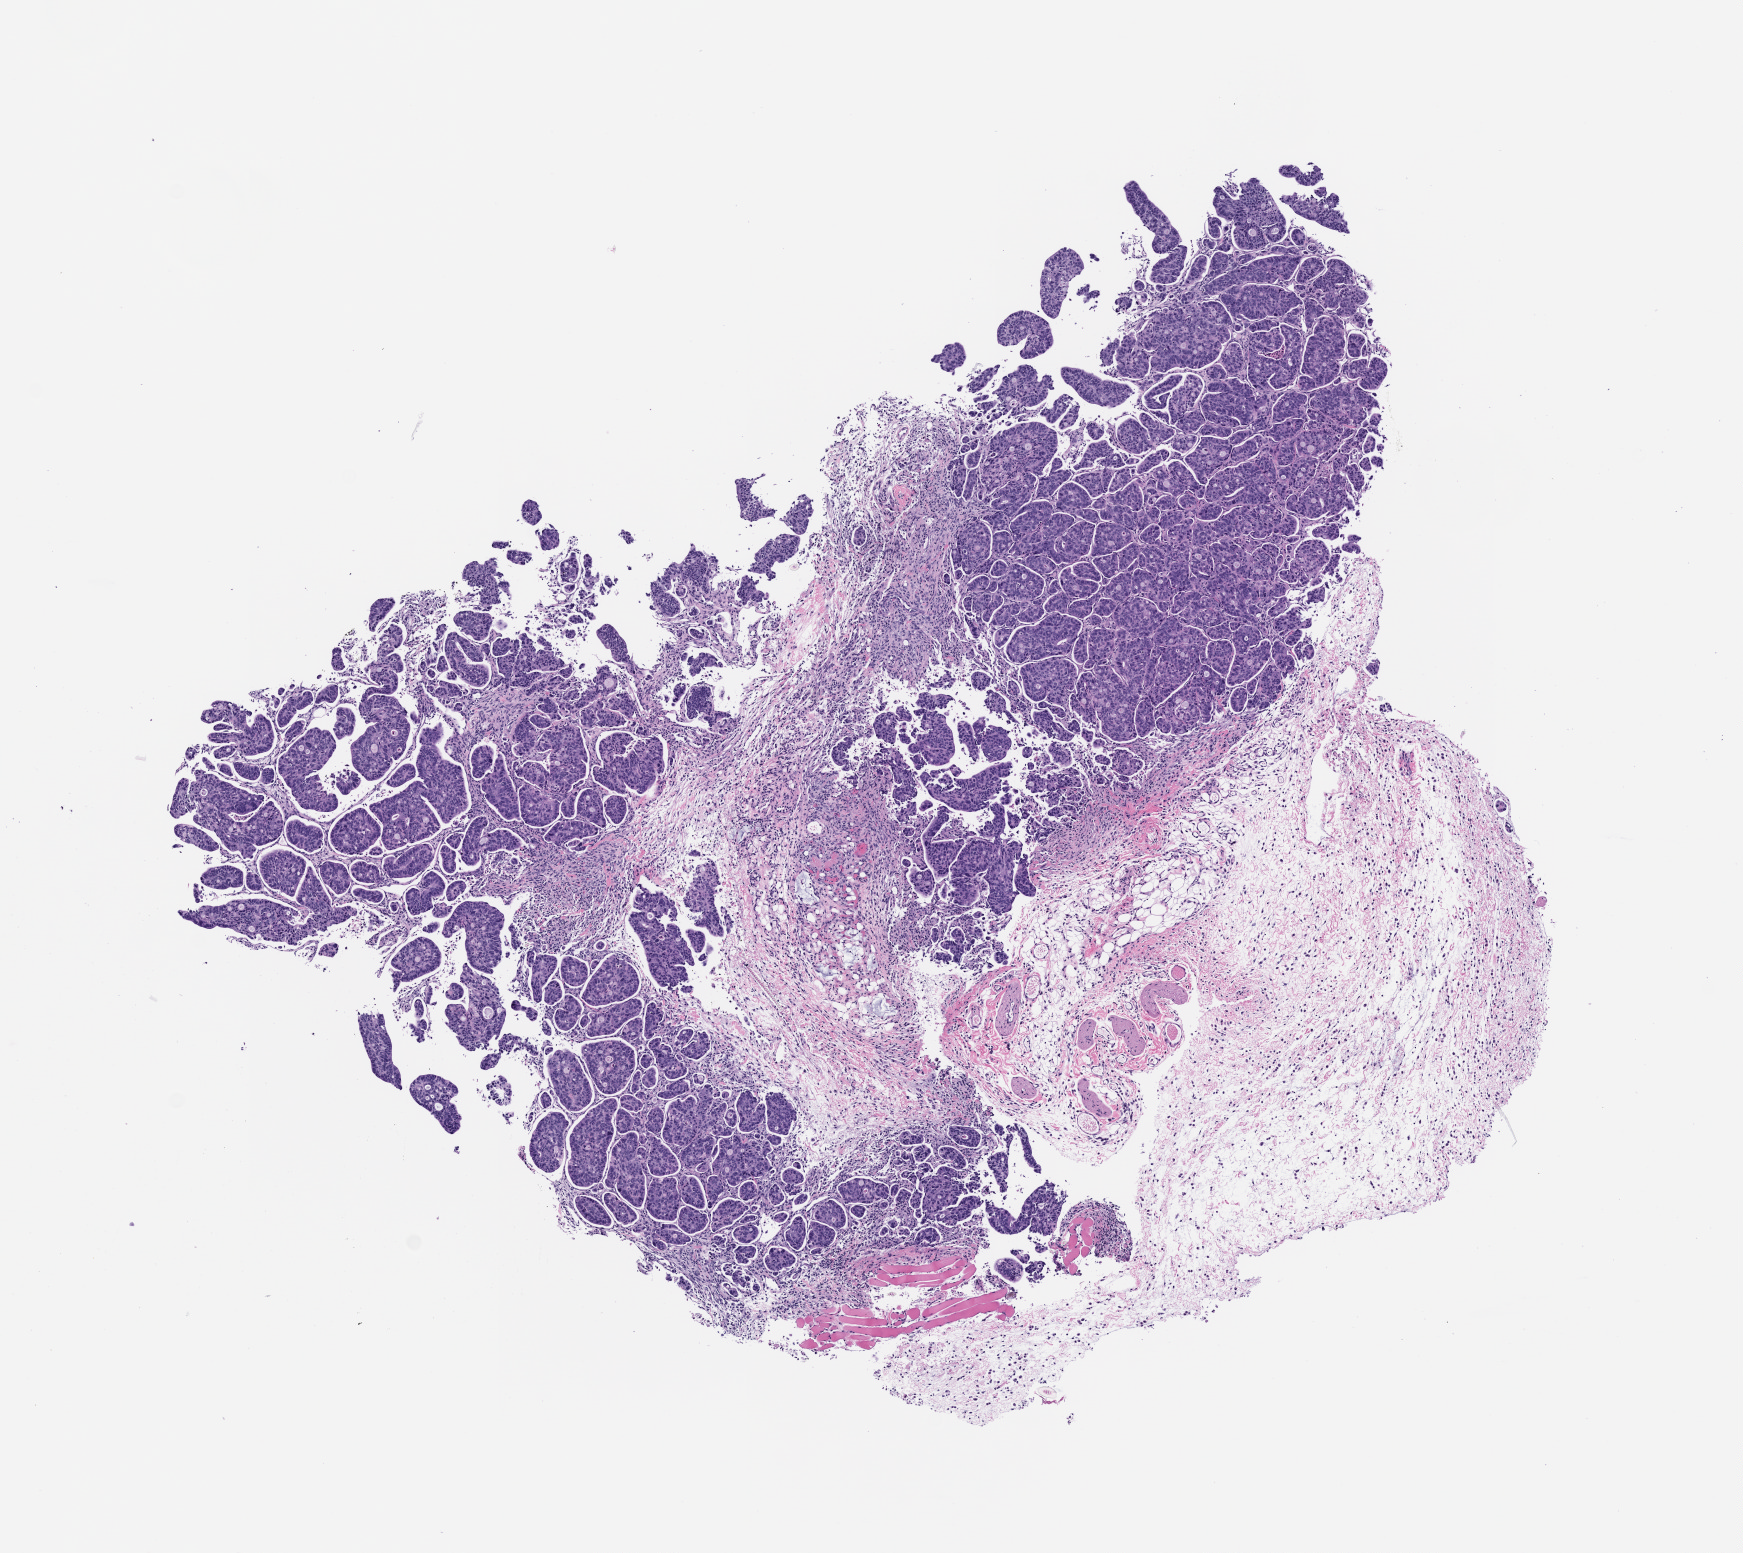
H&E whole-slide image of a patient-derived xenograft (PDX) tumor grown in a mouse, passage 0 — shown as a low-resolution overview of the whole scanned area (about 7.0 x 6.2 mm). Formalin-fixed paraffin-embedded section. Originating tumor site category: colon.
Originating patient diagnosis: Colon Adenocarcinoma.